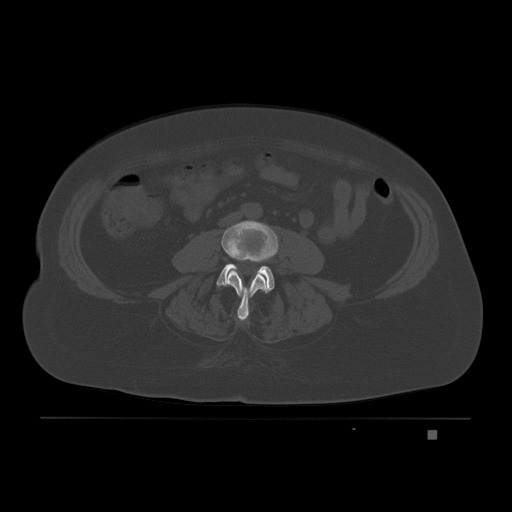
CT including the spine, one axial slice; position 46 of 221 along the scan axis; bone window (W 1800 / L 400 HU); 3 mm slice thickness; 512 × 512 image matrix, field of view 474 × 474 mm. Female patient, age 63 years. Case-level facts recorded for this patient, not image findings: primary cancer: breast.
Annotated regions visible in this slice (semi-automatically segmented with operator editing):
- L3 vertebra: bounding box [x1, y1, x2, y2] px = [221, 220, 279, 321]
- L4 vertebra: [216, 263, 274, 291]